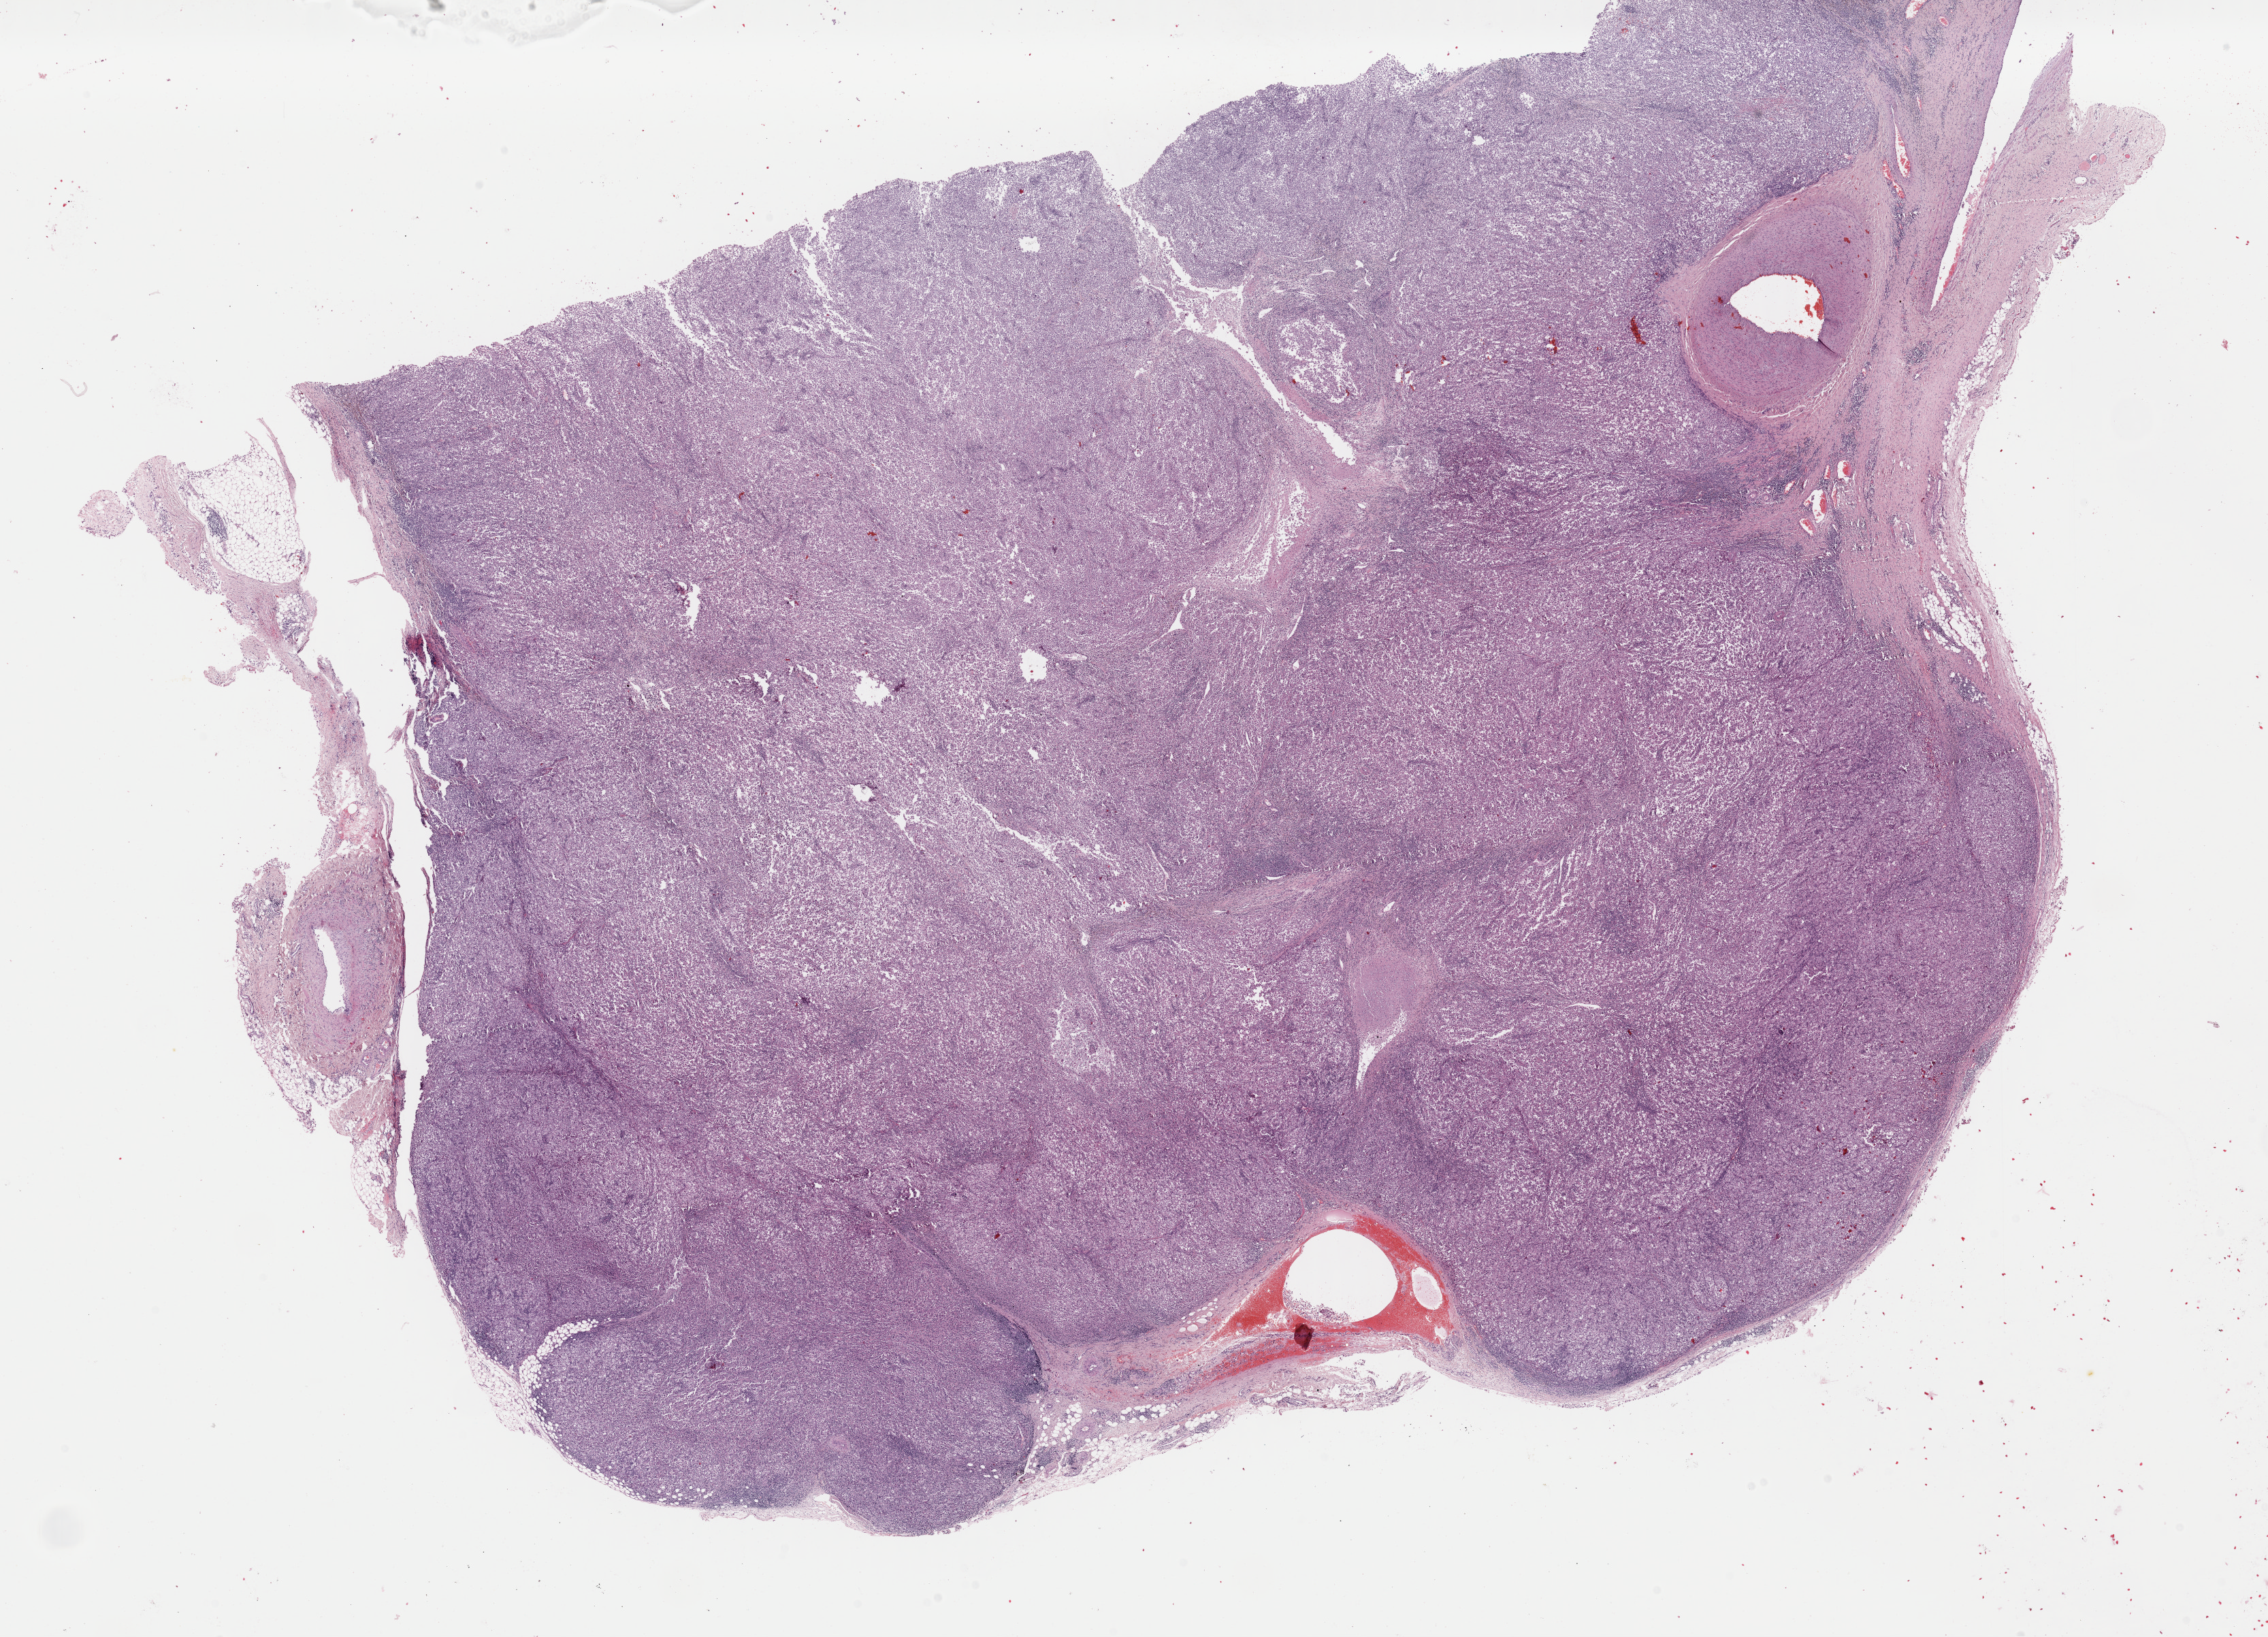
H&E-stained whole-slide image, a low-resolution overview of the entire scanned area, about 26.3 x 19.0 mm. Formalin-fixed paraffin-embedded (FFPE) diagnostic section. Metastatic tumour sample, sampled site: lymph nodes of axilla or arm. Male, age 66 years at initial diagnosis.
This section: metastatic tumour tissue. Patient diagnosis: Malignant melanoma, NOS.